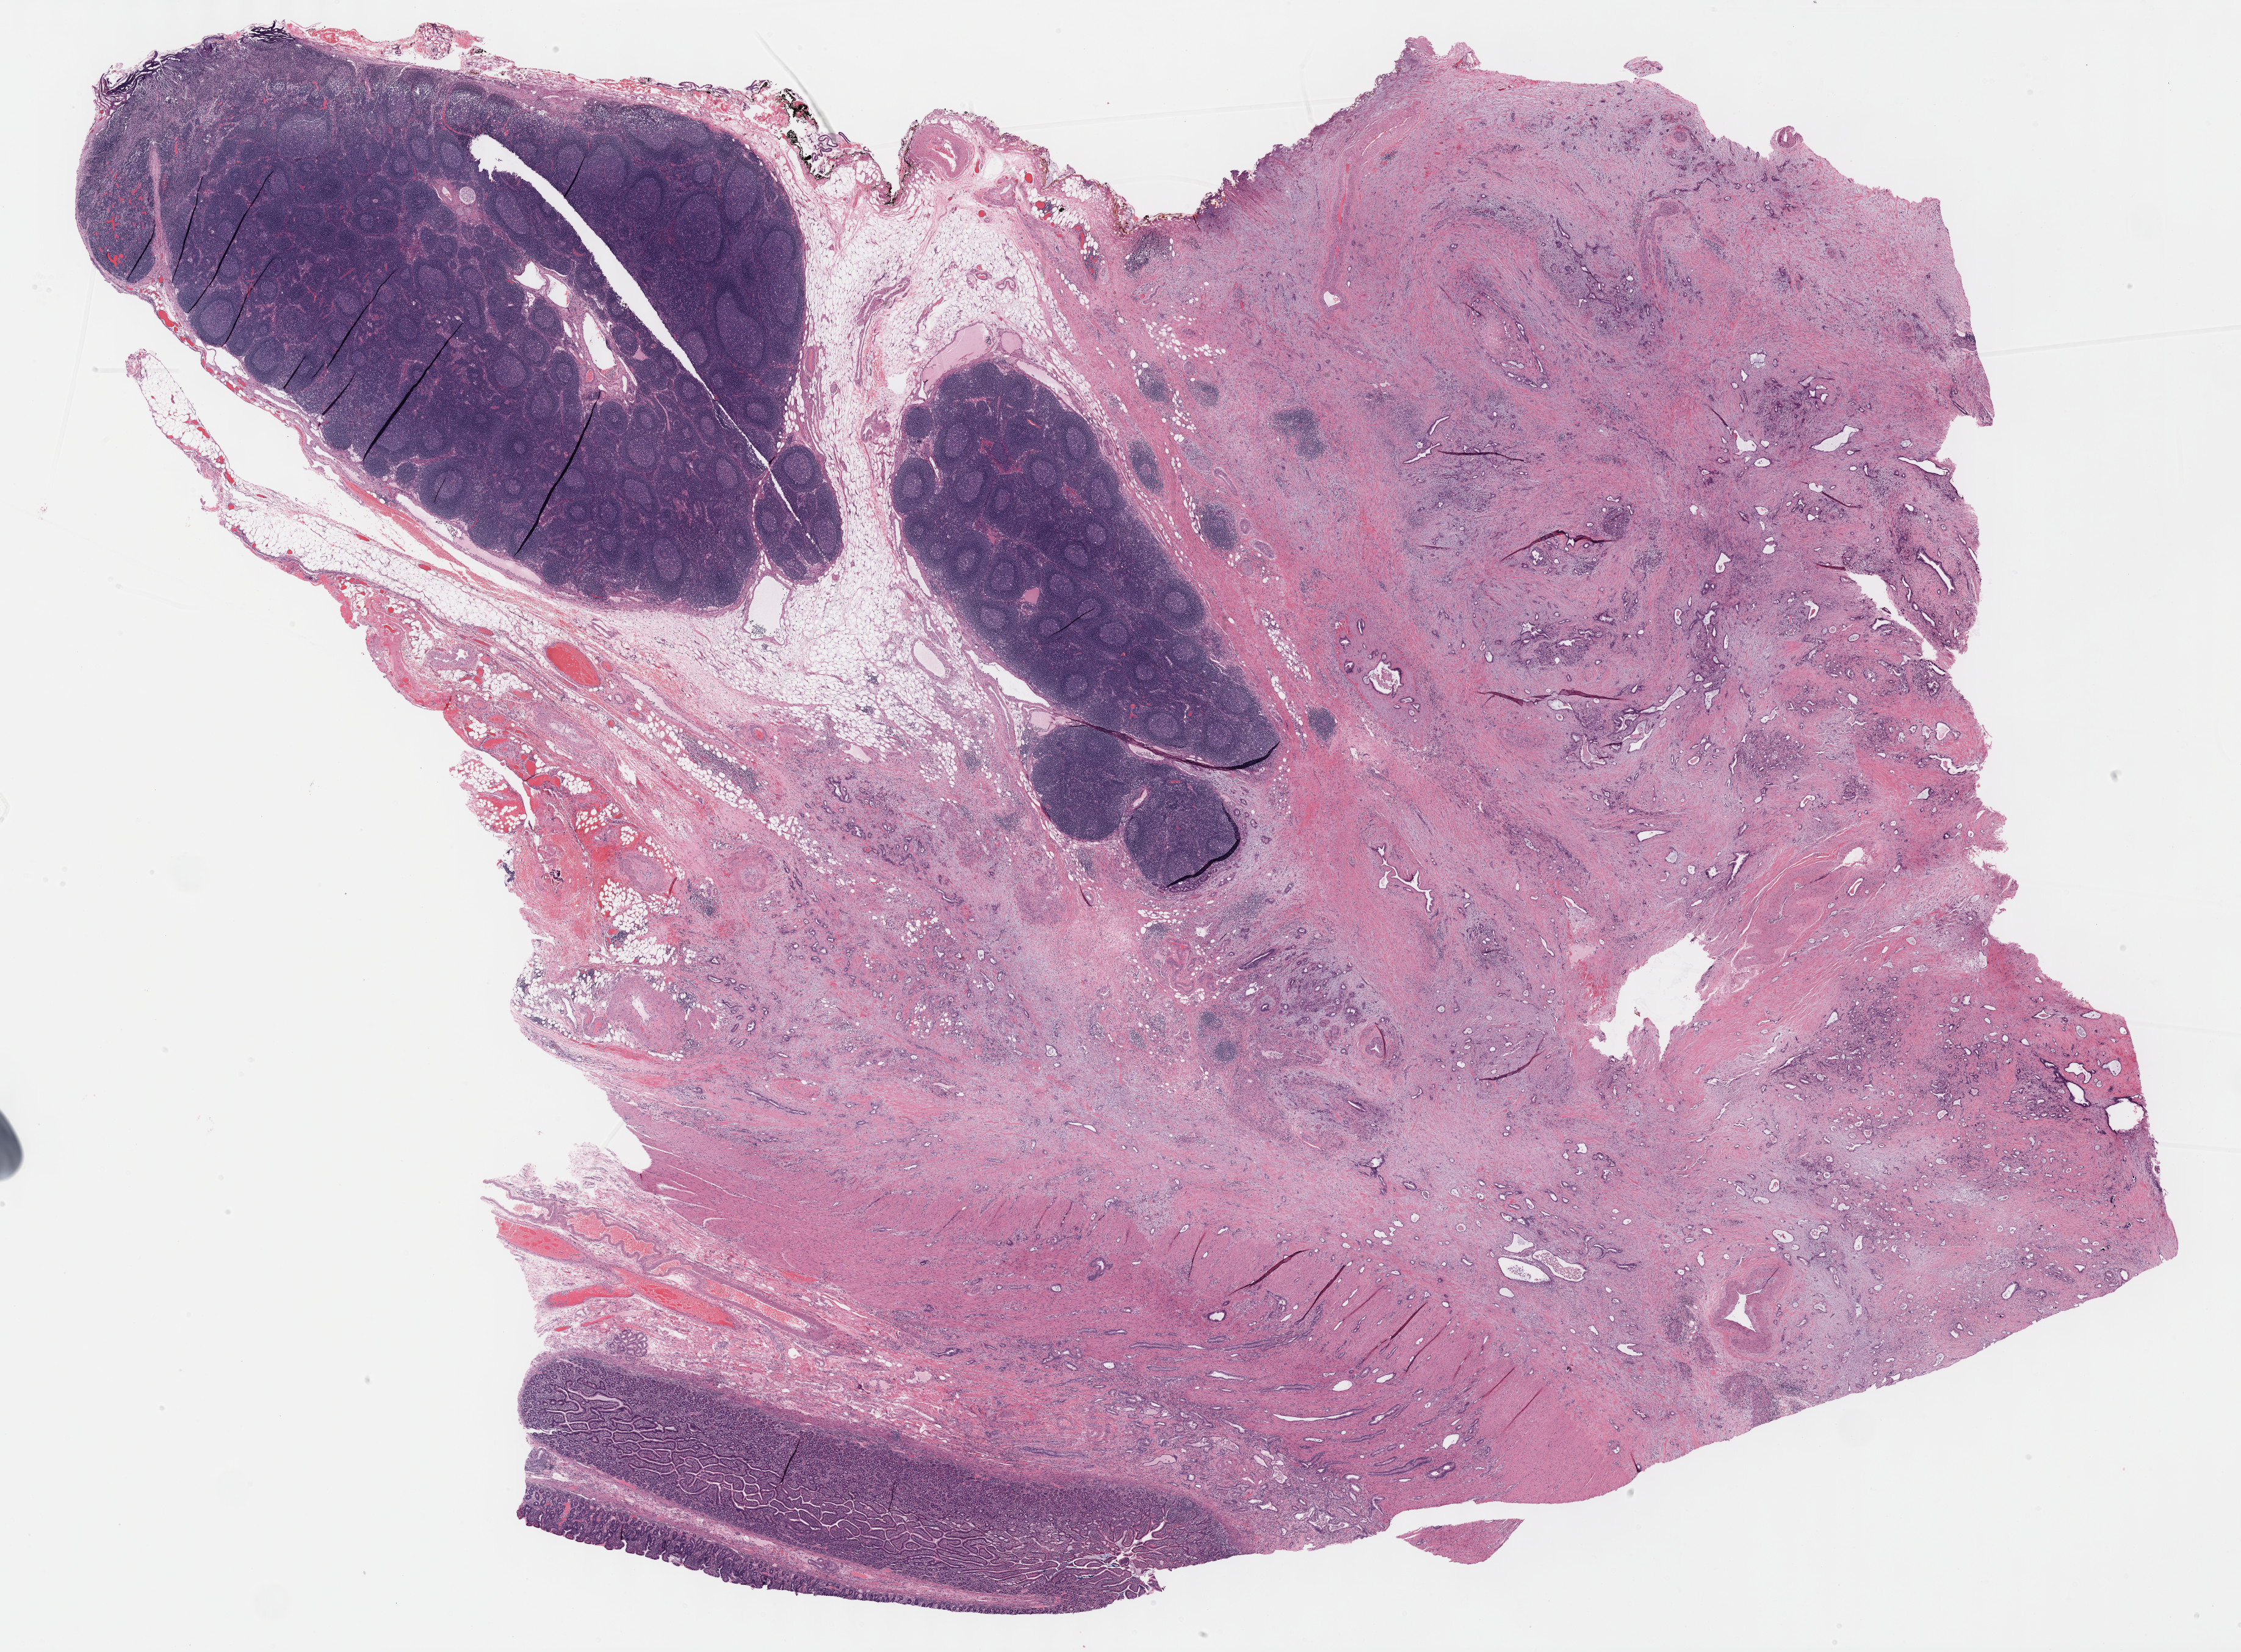
Whole-slide histology image, H&E — low-resolution overview of the scanned area, about 29.7 x 21.9 mm (slide scanned at 40x), formalin-fixed paraffin-embedded (FFPE) diagnostic section, pancreas, primary tumour sample. Male, age 68 years at initial diagnosis. Histologic grade: G2 (moderately differentiated).
- TNM: T3 N1 M0
- diagnosis: Infiltrating duct carcinoma, NOS
- AJCC pathologic stage: IIB (7th edition)
- lymph nodes positive (case pathology): 7 of 21 examined